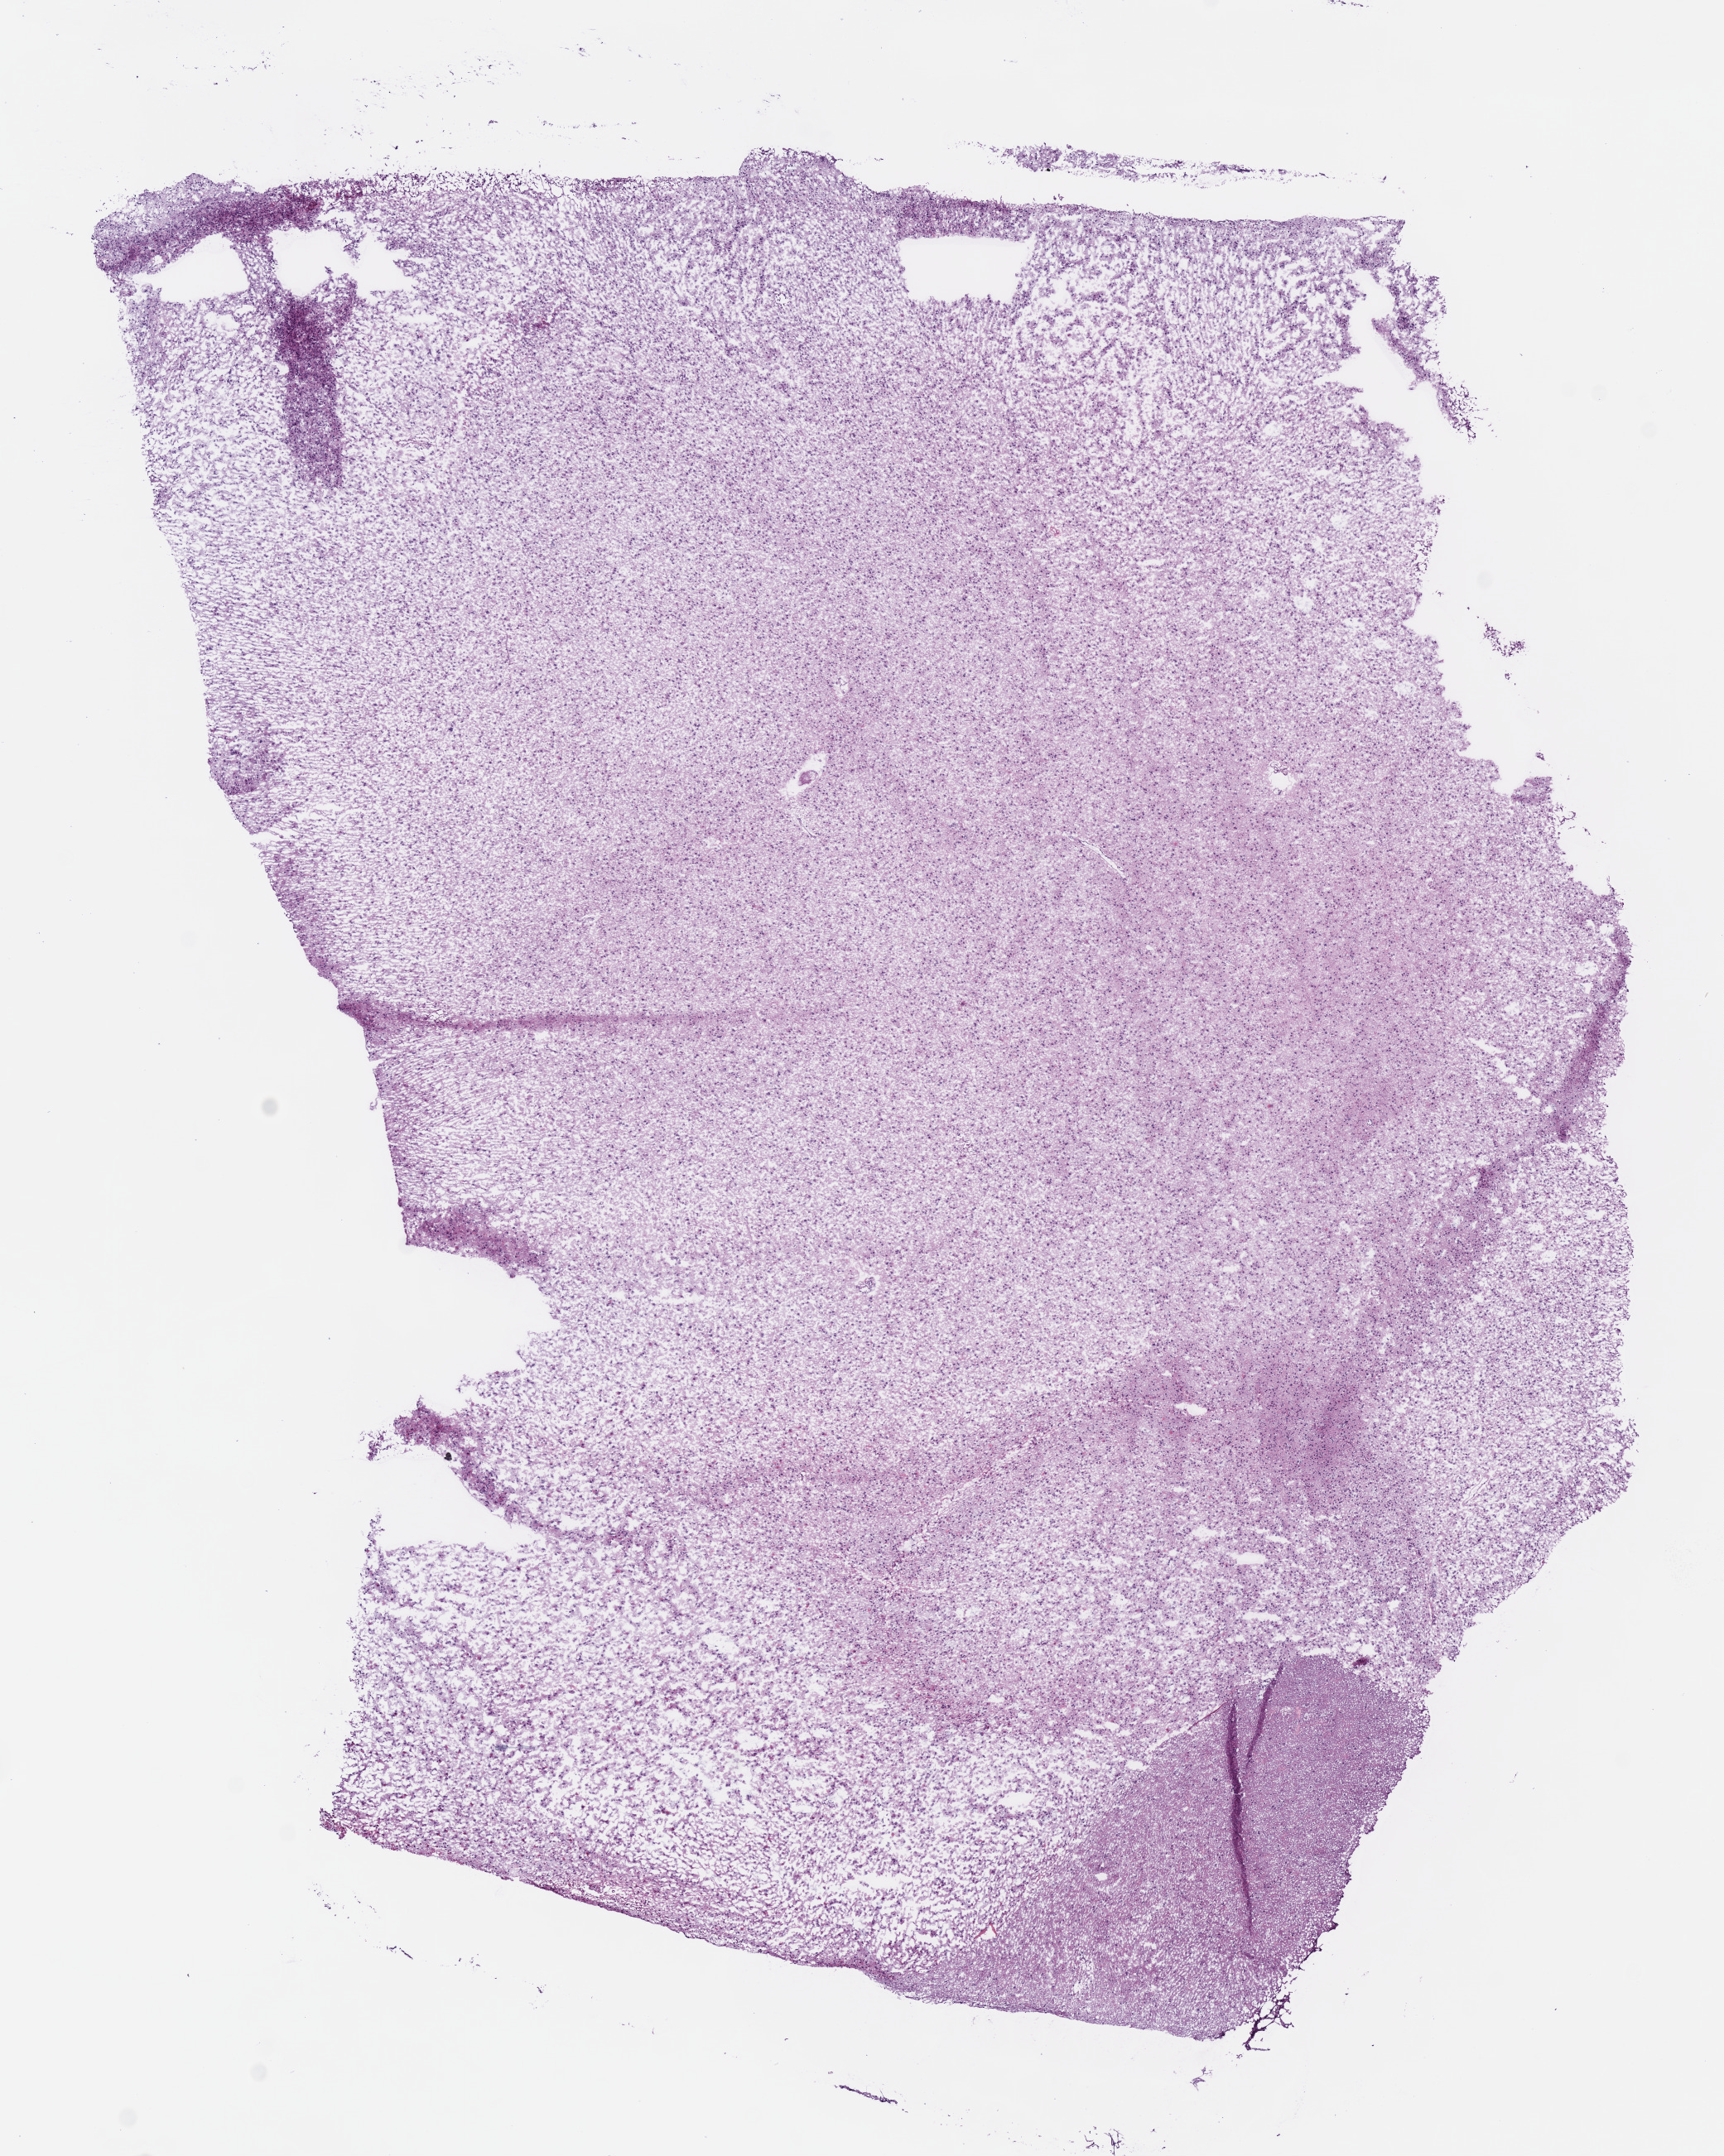
Whole-slide histology image, H&E-stained, shown as a low-resolution overview of the whole scanned area (about 8.2 x 10.3 mm, from a 40x scan), frozen section, brain, primary tumour sample. Patient: male, age at initial diagnosis 36 years. Histologic grade: G2 (moderately differentiated). Pathologist review of this section (percent, as recorded): tumour cells 100%, tumour nuclei 80%, normal cells 0%, stromal cells 0%, necrosis 0%.
• pathologic diagnosis: Mixed glioma (cerebrum)
• laterality: right